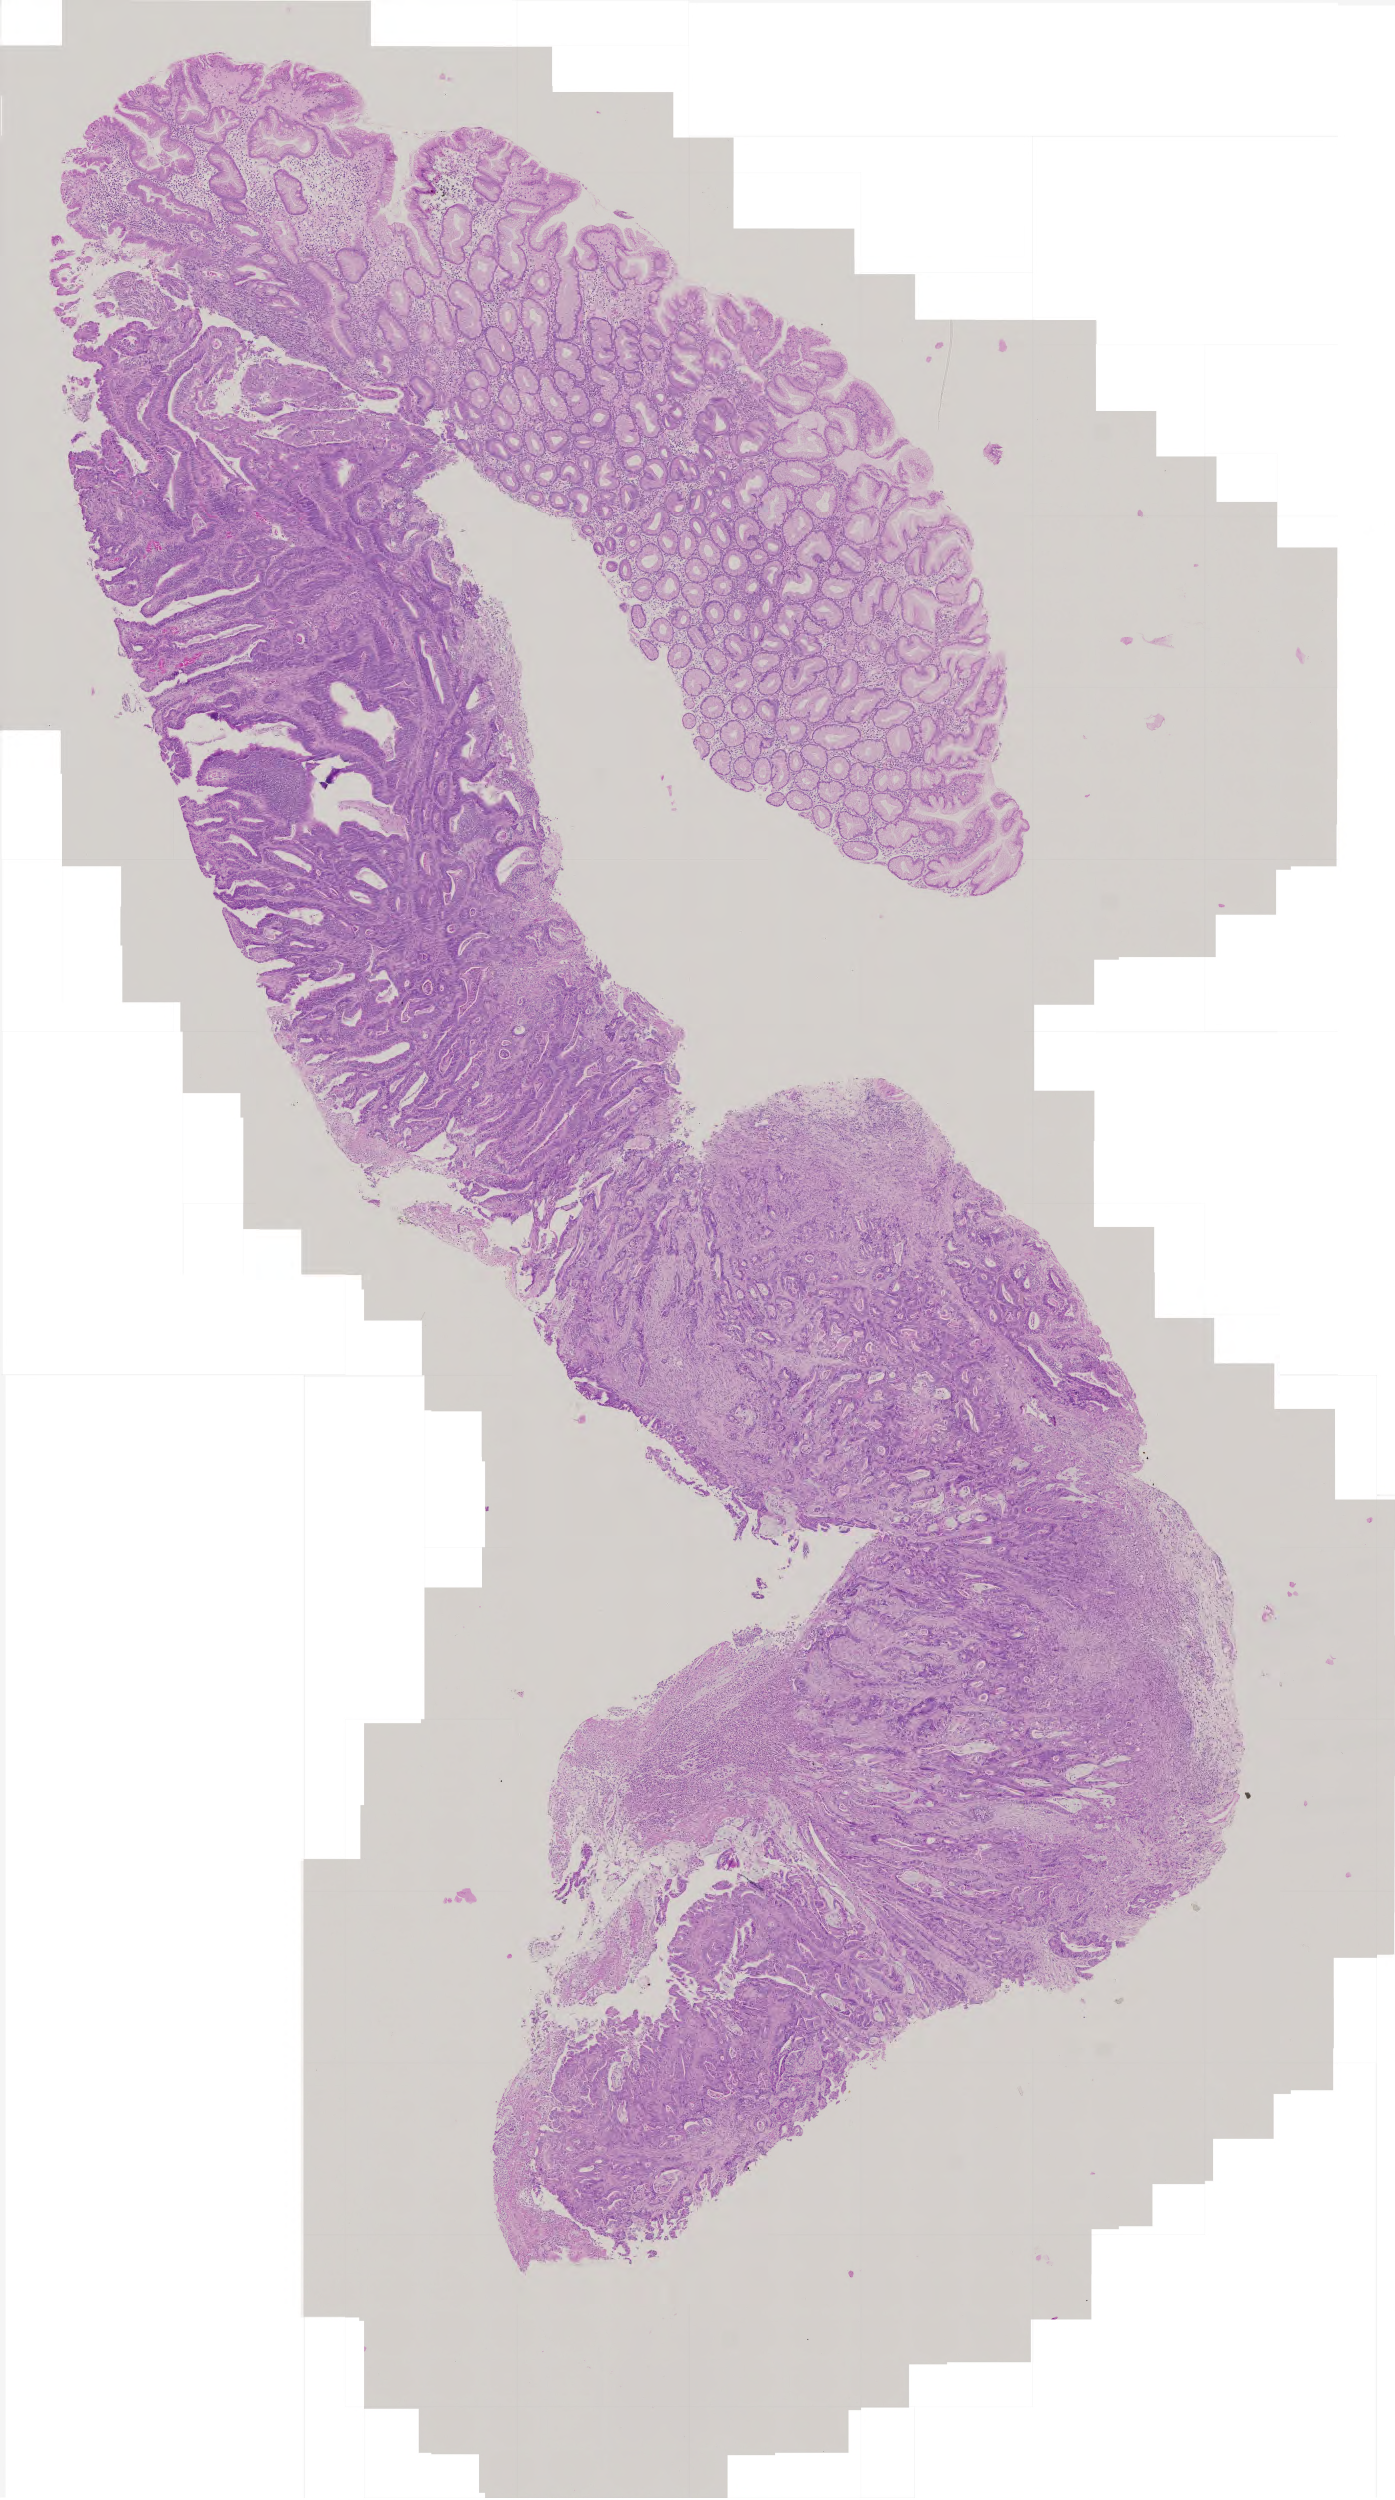
Digitized H&E-stained tissue section (whole slide), shown as a low-resolution overview of the whole scanned area (about 2.8 x 5.0 mm); formalin-fixed paraffin-embedded (FFPE) diagnostic section; stomach, primary tumour sample. Patient sex: female.
Pathologic diagnosis: Adenocarcinoma, intestinal type (gastric antrum).